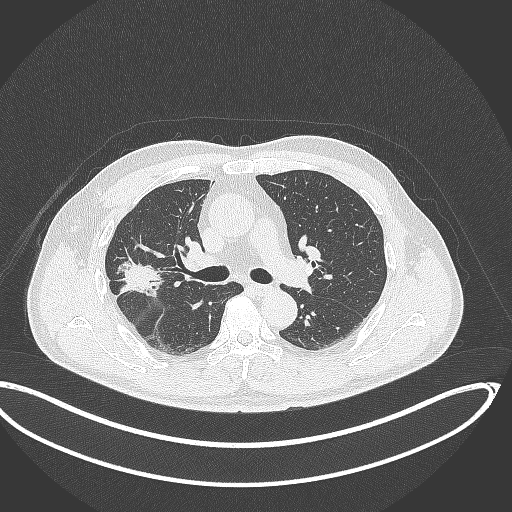
Chest CT, one axial slice; slice 210 of 391 in the series (ordered by position); 120 kVp; lung window (W 1500 / L -600 HU); 512 × 512 image matrix, field of view 439 × 439 mm. Male patient, age 63 years. Case-level facts recorded for this patient, not image findings: clinical TNM (as recorded): T1c N0 M0.
Outlined on this slice (bounding box drawn by a radiologist):
- lung tumour (recorded histology: adenocarcinoma): bounding box <112,253,166,301> (left, top, right, bottom; pixels)